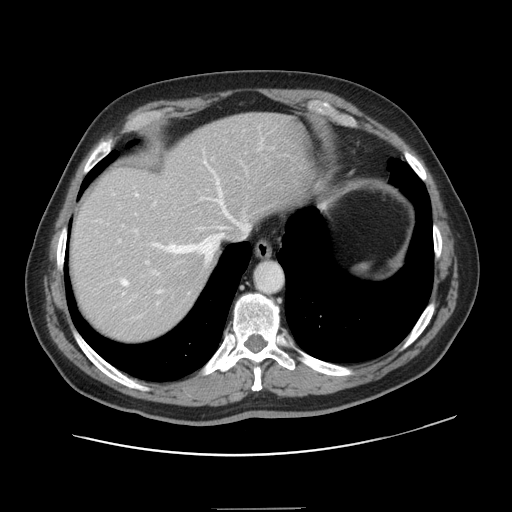
Contrast-enhanced abdominal CT, one axial slice. Position 120 of 143 along the scan axis. 120 kVp. Intravenous contrast given. Soft-tissue window (W 400 / L 40 HU). 2.5 mm slice thickness. 512 × 512 image matrix, field of view 402 × 402 mm. Male patient, age 62 years. Case-level facts recorded for this patient, not image findings: diagnosis: colorectal cancer liver metastases, imaged before liver resection.
Annotated regions visible in this slice (outlined manually by an expert reader):
- hepatic veins: bounding box [x1, y1, x2, y2] px = [121, 179, 247, 304]
- liver: [72, 114, 307, 341]
- planned liver remnant (the part of the liver to remain after resection): [72, 114, 307, 290]
- portal vein (with intrahepatic branches): [119, 203, 158, 275]